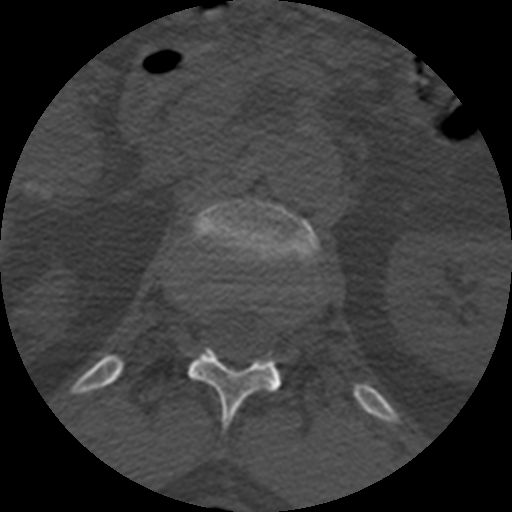
CT including the spine, one axial slice; slice 378 of 399 in the series (ordered by position); reconstruction kernel STANDARD; bone window (W 1800 / L 400 HU); 1.25 mm slice thickness; 512 × 512 image matrix, field of view 160 × 160 mm. Patient age 71 years. Case-level facts recorded for this patient, not image findings: primary cancer: prostate.
Annotated regions visible in this slice (semi-automatic segmentation, software-assisted and operator-edited):
- L1 vertebra: bounding box <190,199,320,266> (left, top, right, bottom; pixels)
- T12 vertebra: <187,349,282,433>